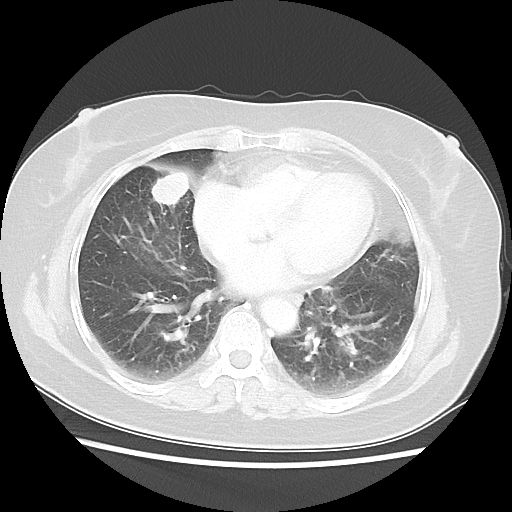
Chest CT, one axial slice. Slice 20 of 48 in the series (ordered by position). Reconstruction kernel LUNG. 100 kVp. Lung window (W 1500 / L -600 HU). 512 × 512 image matrix, field of view 343 × 343 mm. Female patient, age 61 years. From the clinical record (not read from this slice): clinical TNM (as recorded): T1c N0 M0.
Outlined on this slice (bounding box drawn by a radiologist):
- lung tumour (recorded histology: adenocarcinoma): bounding box <148,169,189,208> (left, top, right, bottom; pixels)